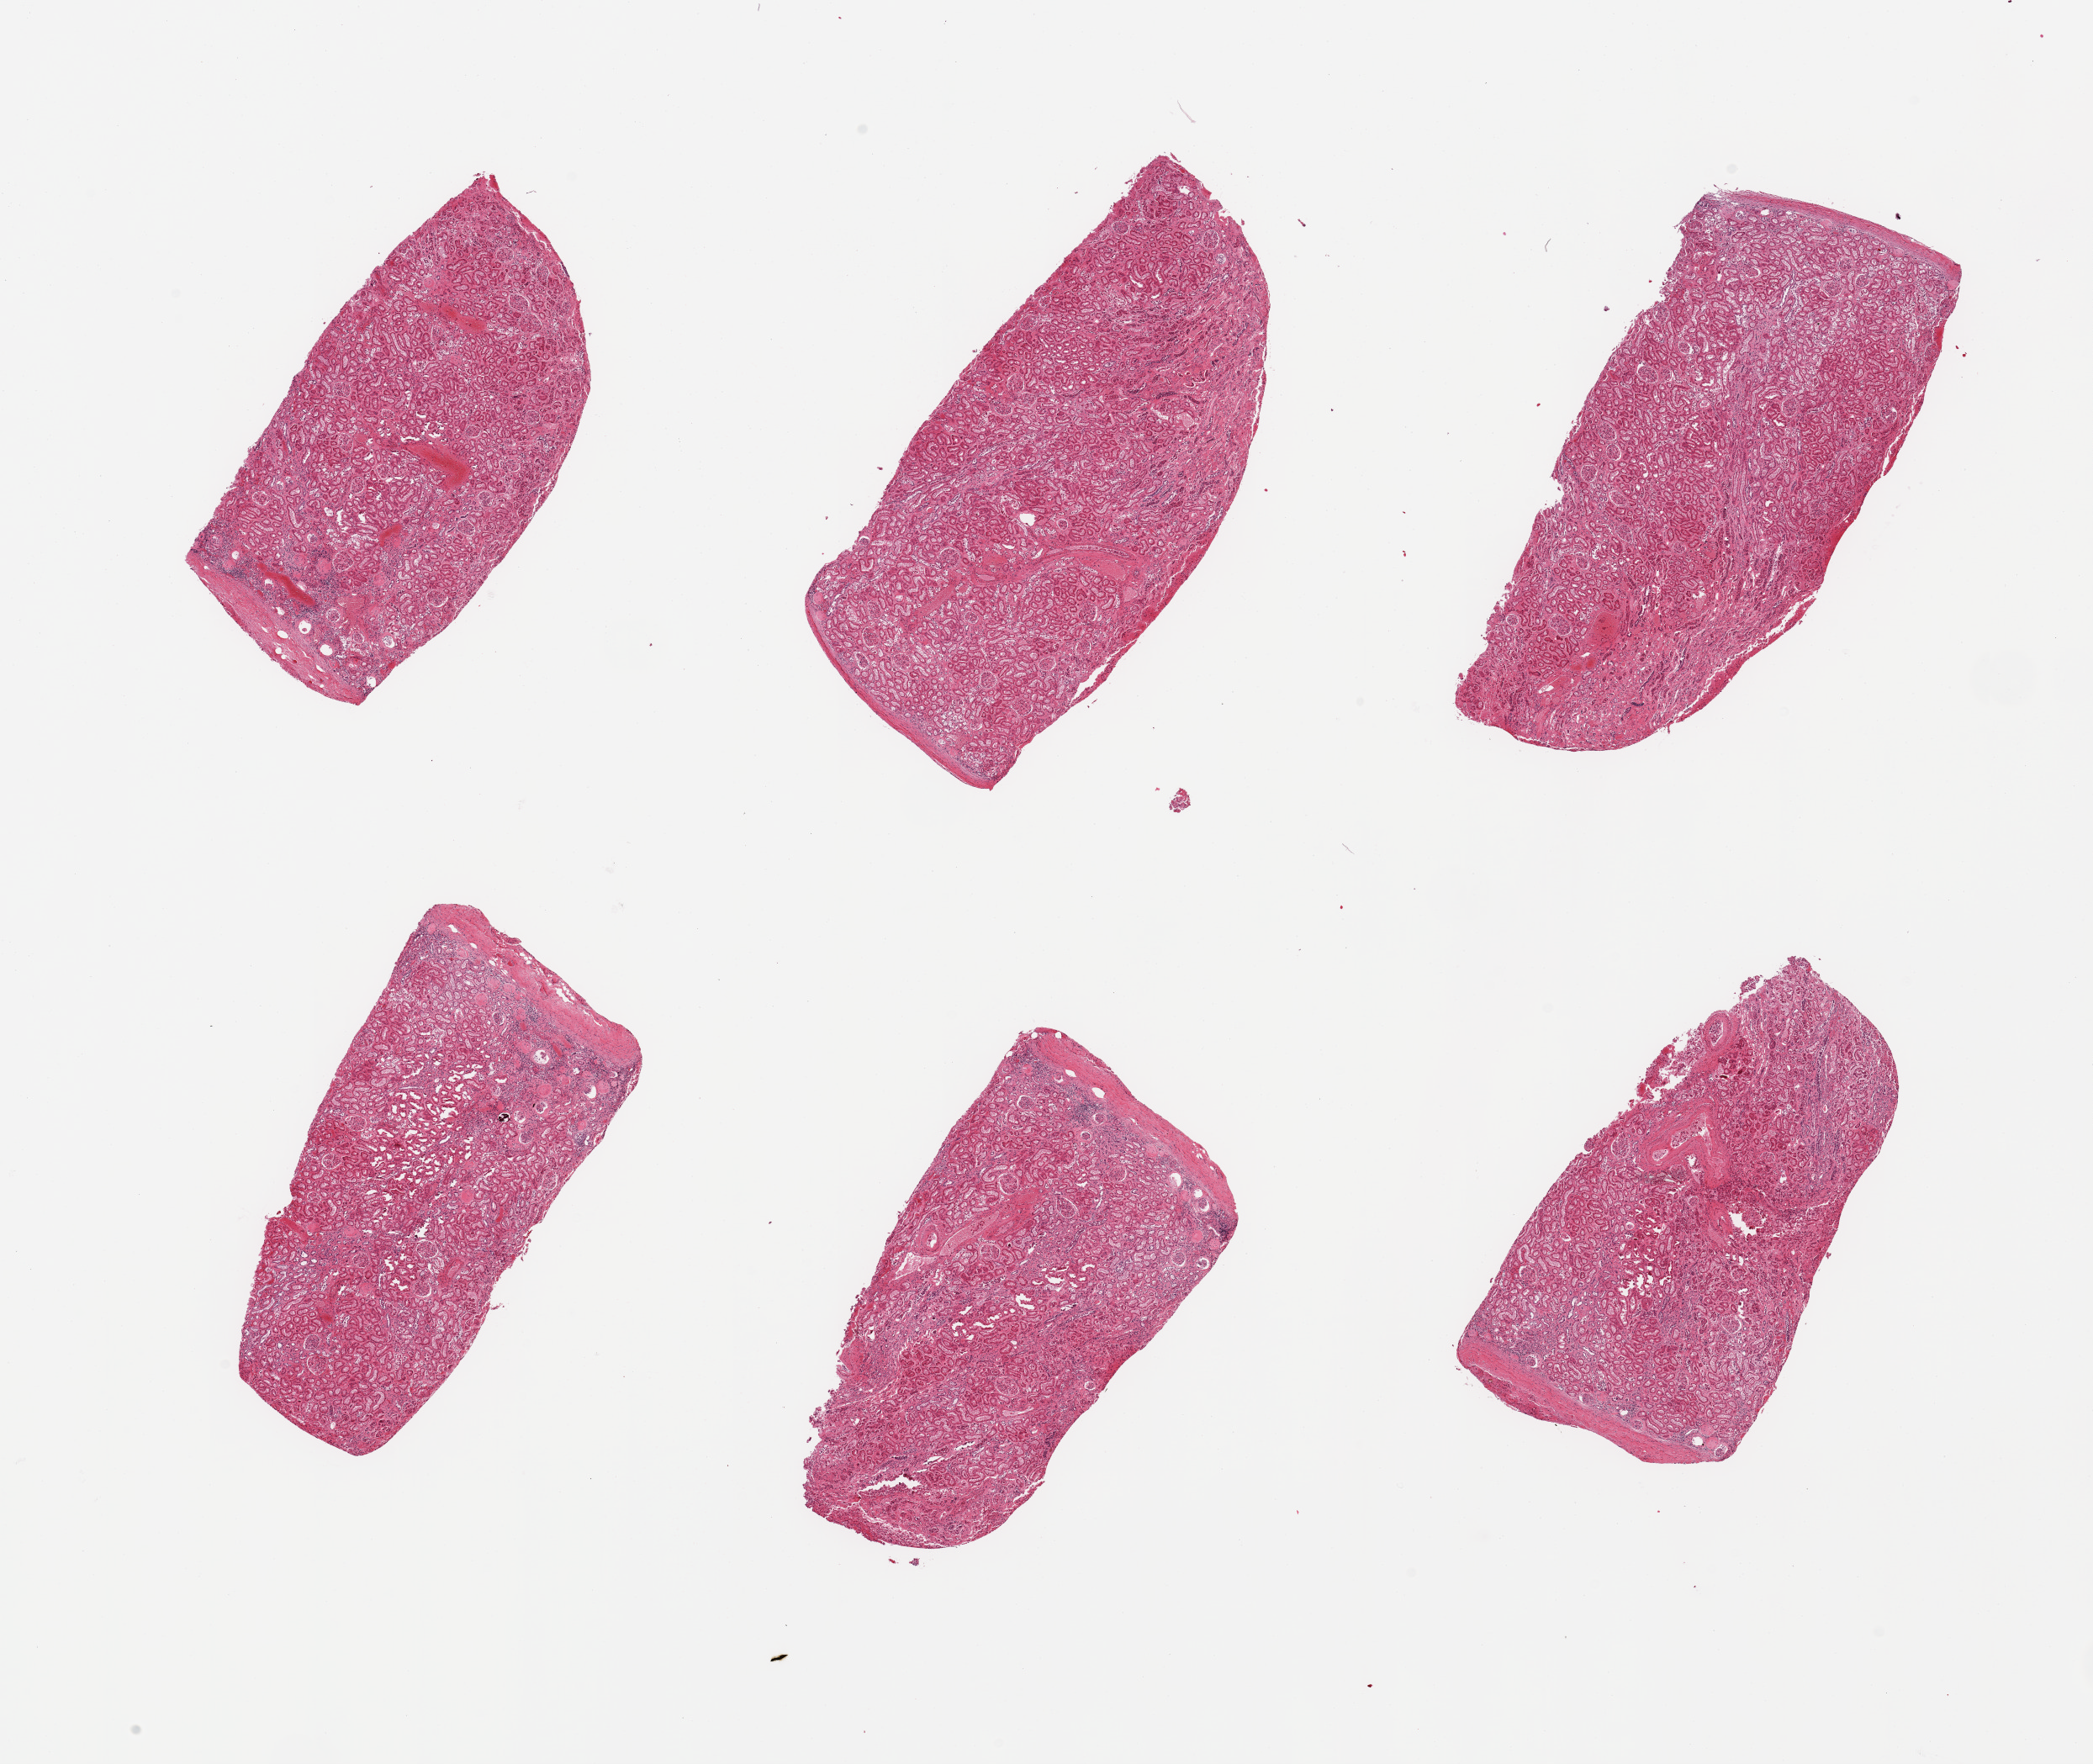
Digitized haematoxylin and eosin-stained section — a low-resolution overview of the entire scanned area, about 19.7 x 16.6 mm (slide scanned at 20x); PAXgene-fixed, paraffin-embedded tissue; sampled site (target tissue): renal cortex; tissue donor sample. Donor: female.
Review note (as recorded): 6 pieces; no chronic disease.